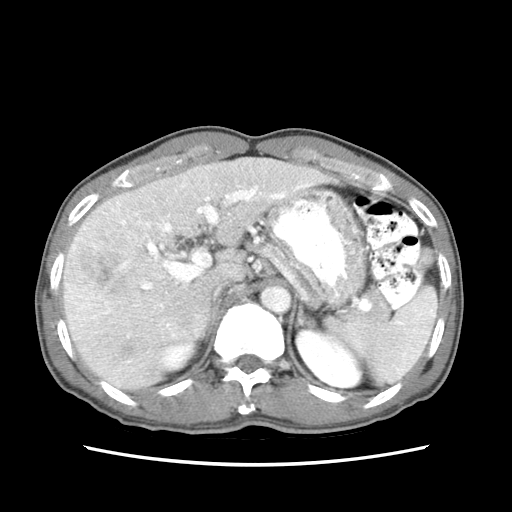
Contrast-enhanced abdominal CT (liver protocol), one axial slice. Slice 46 of 79 in the series (ordered by position). 120 kVp. Soft-tissue window (W 400 / L 40 HU). 512 × 512 image matrix. Case-level facts recorded for this patient, not image findings: diagnosis: hepatocellular carcinoma (patient treated with transarterial chemoembolisation; whether this scan precedes or follows treatment is not stated here); TNM stage (as recorded): Stage-IIIB; Child-Pugh class: A.
Annotated regions visible in this slice (semi-automatically segmented with operator editing):
- liver parenchyma outside the tumour (the mass and vessels are separate outlines, so this box may not span the whole liver): bounding box <62,156,350,390> (left, top, right, bottom; pixels)
- mass: <63,227,131,320>
- liver vessels: <67,168,311,362>